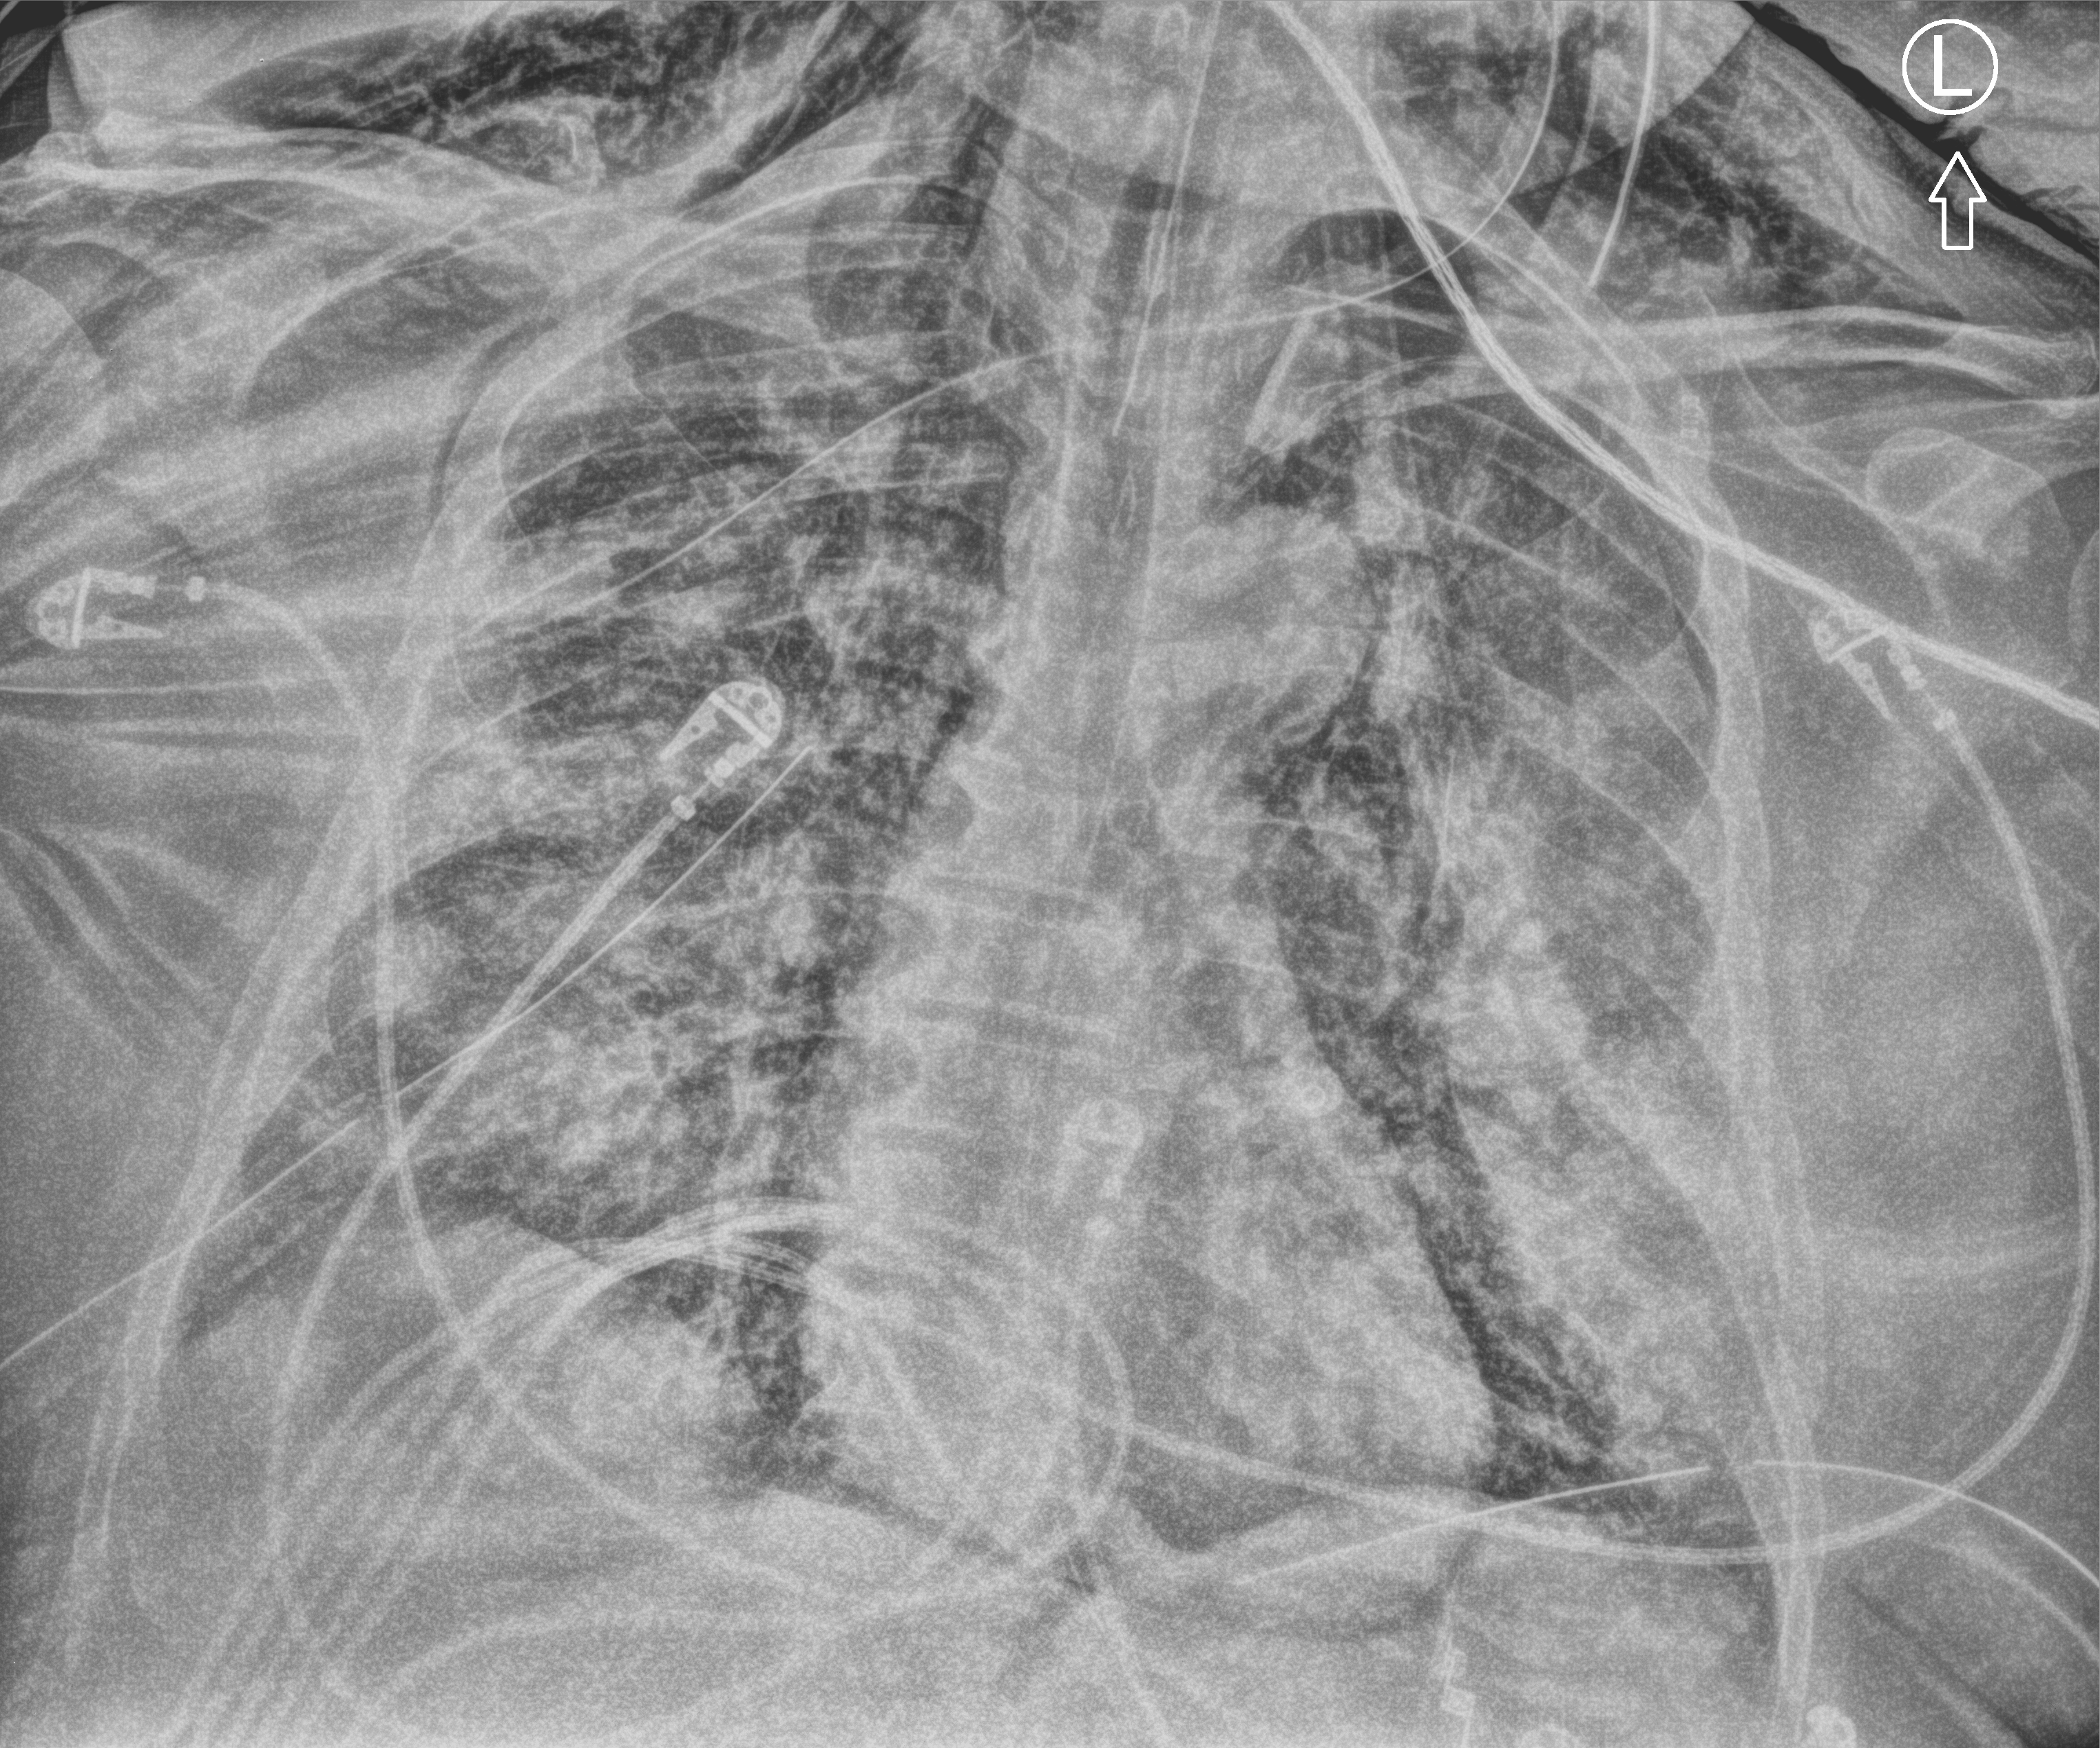
Portable chest radiograph. Adult patient hospitalised with COVID-19, age 18–59 years.
Hospital-stay facts (about this admission, not read from this image; timing relative to this image not recorded):
- mechanically ventilated during this hospital stay: yes
- diabetes (admission record): no
- length of hospital stay: 28 days